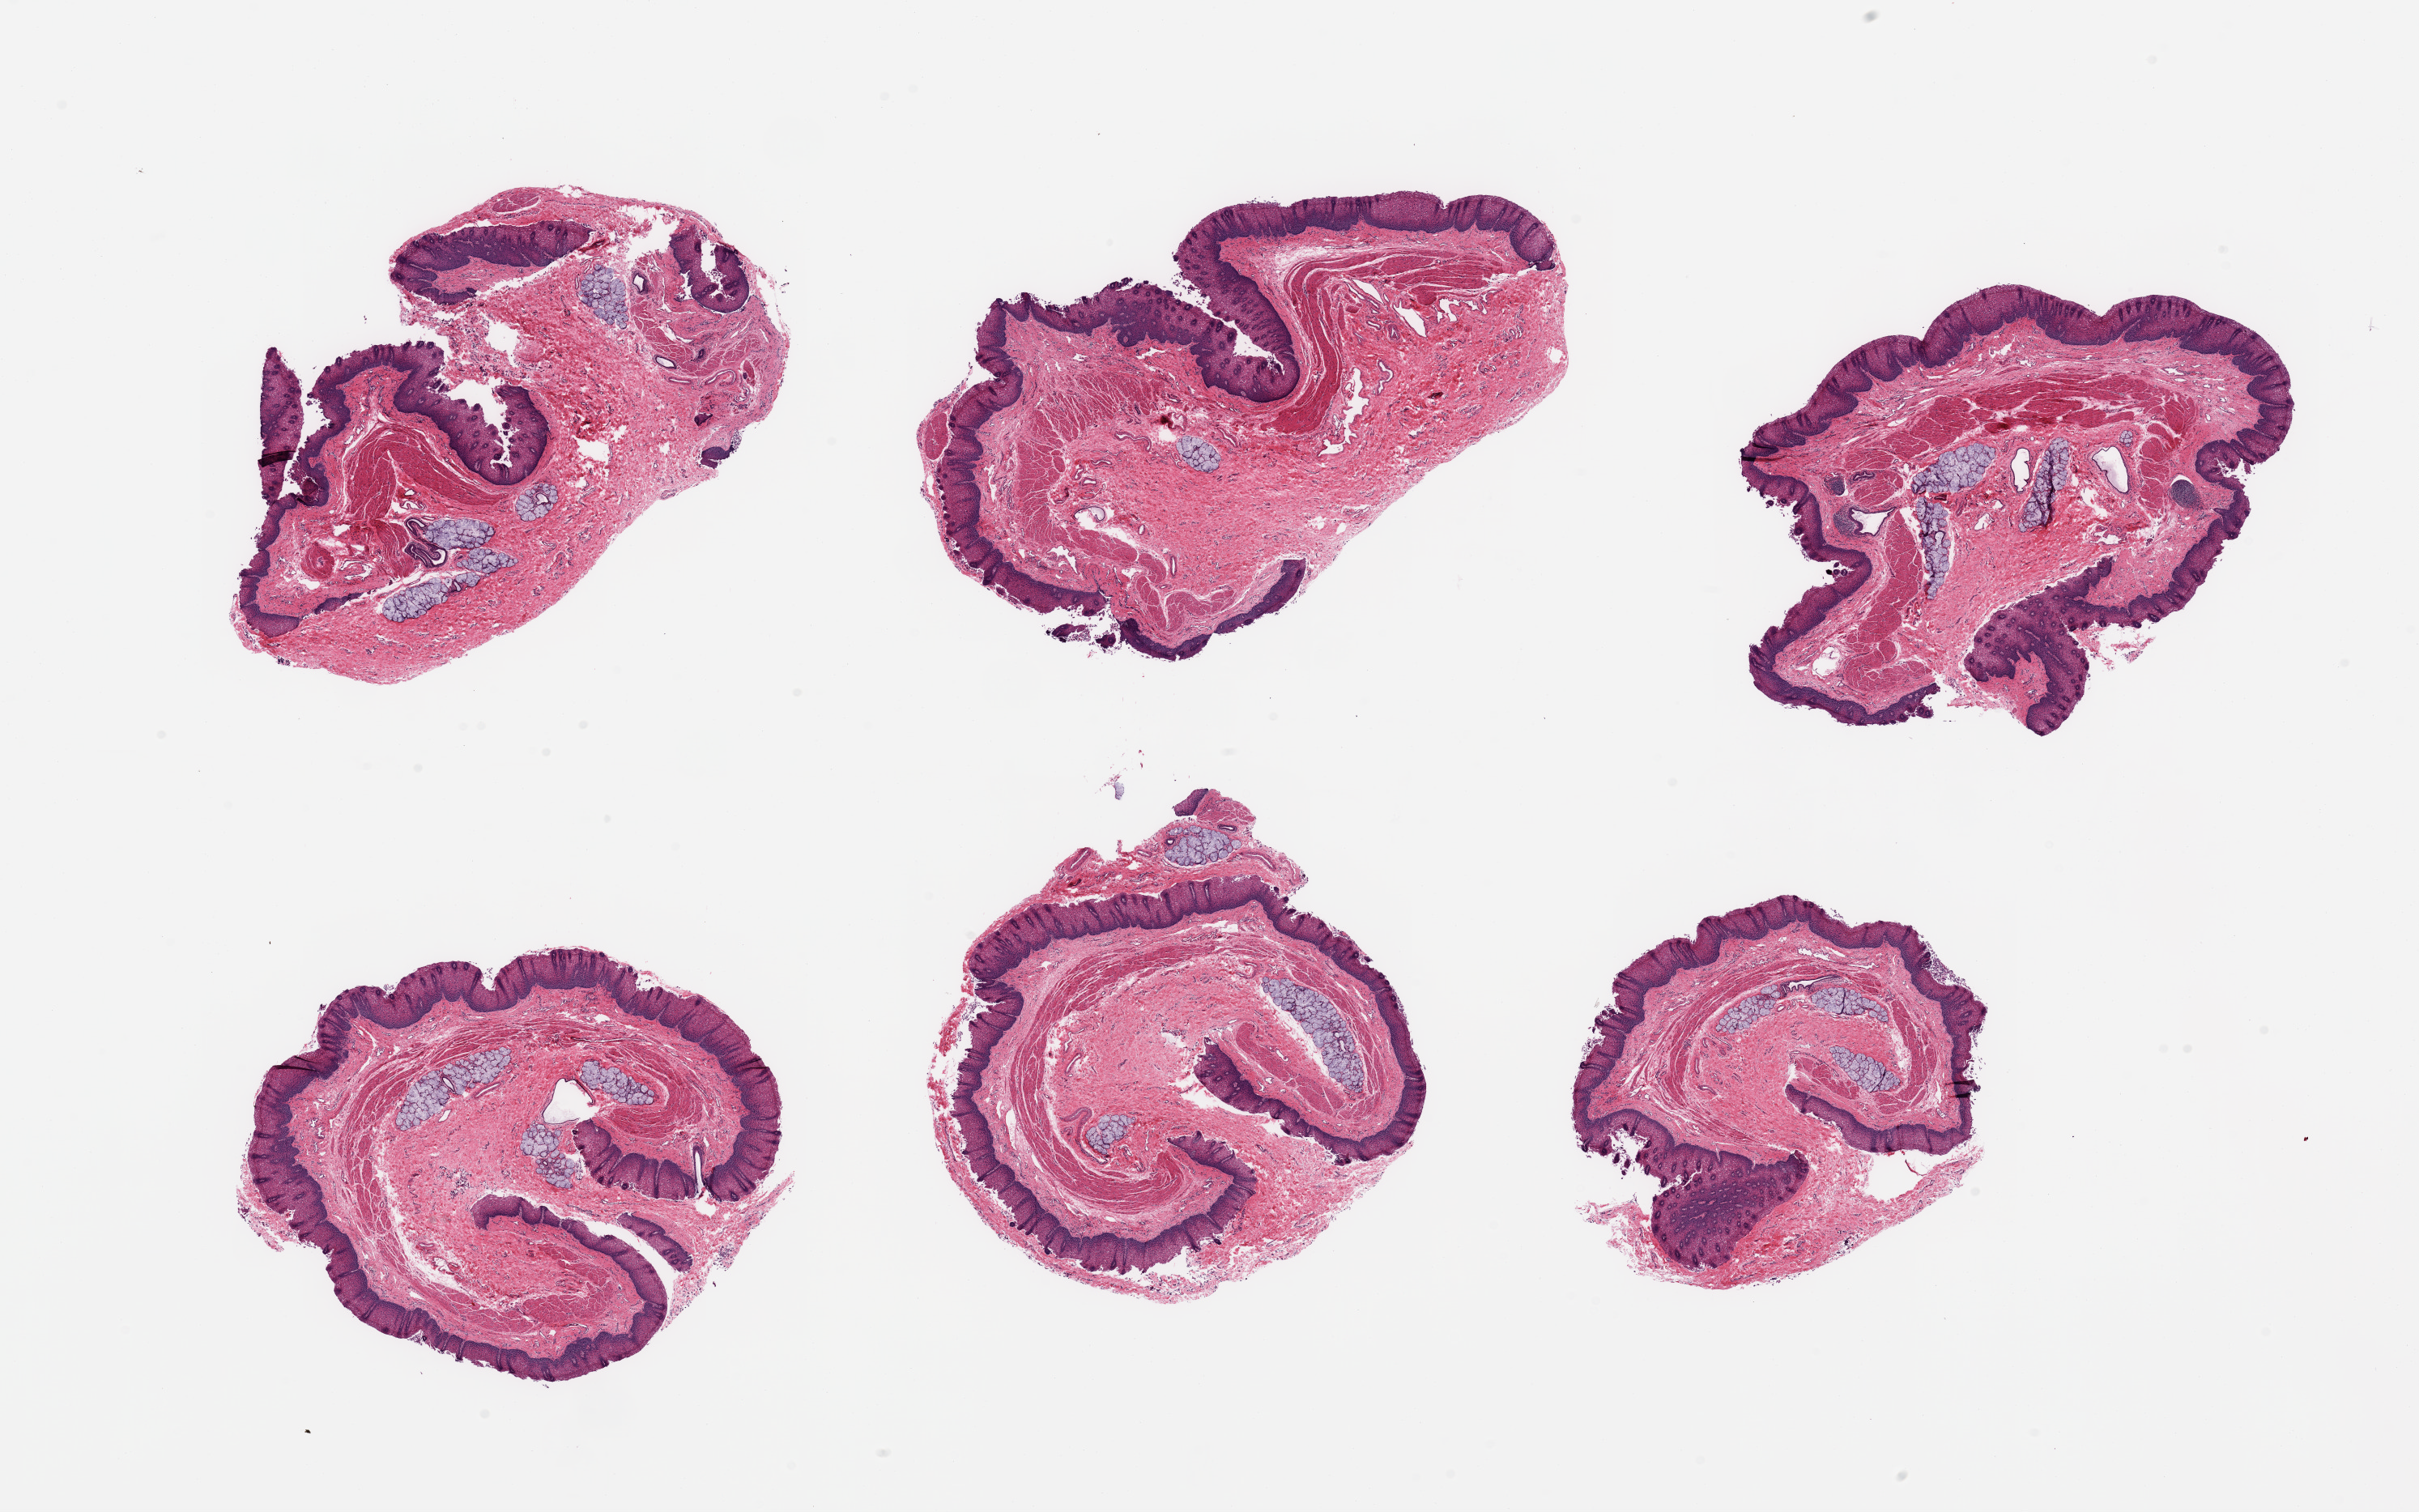
Digitized haematoxylin and eosin-stained section — whole scanned area (about 23.6 x 14.8 mm, acquisition: 20x scan) shown as a low-resolution overview; PAXgene-fixed, paraffin-embedded tissue; target tissue: esophageal mucous membrane; tissue donor sample.
Review note (as recorded): 6 pieces; mild to focally moderate autolysis; ~0.3mm thick epithelium: numerous submucosal glands.